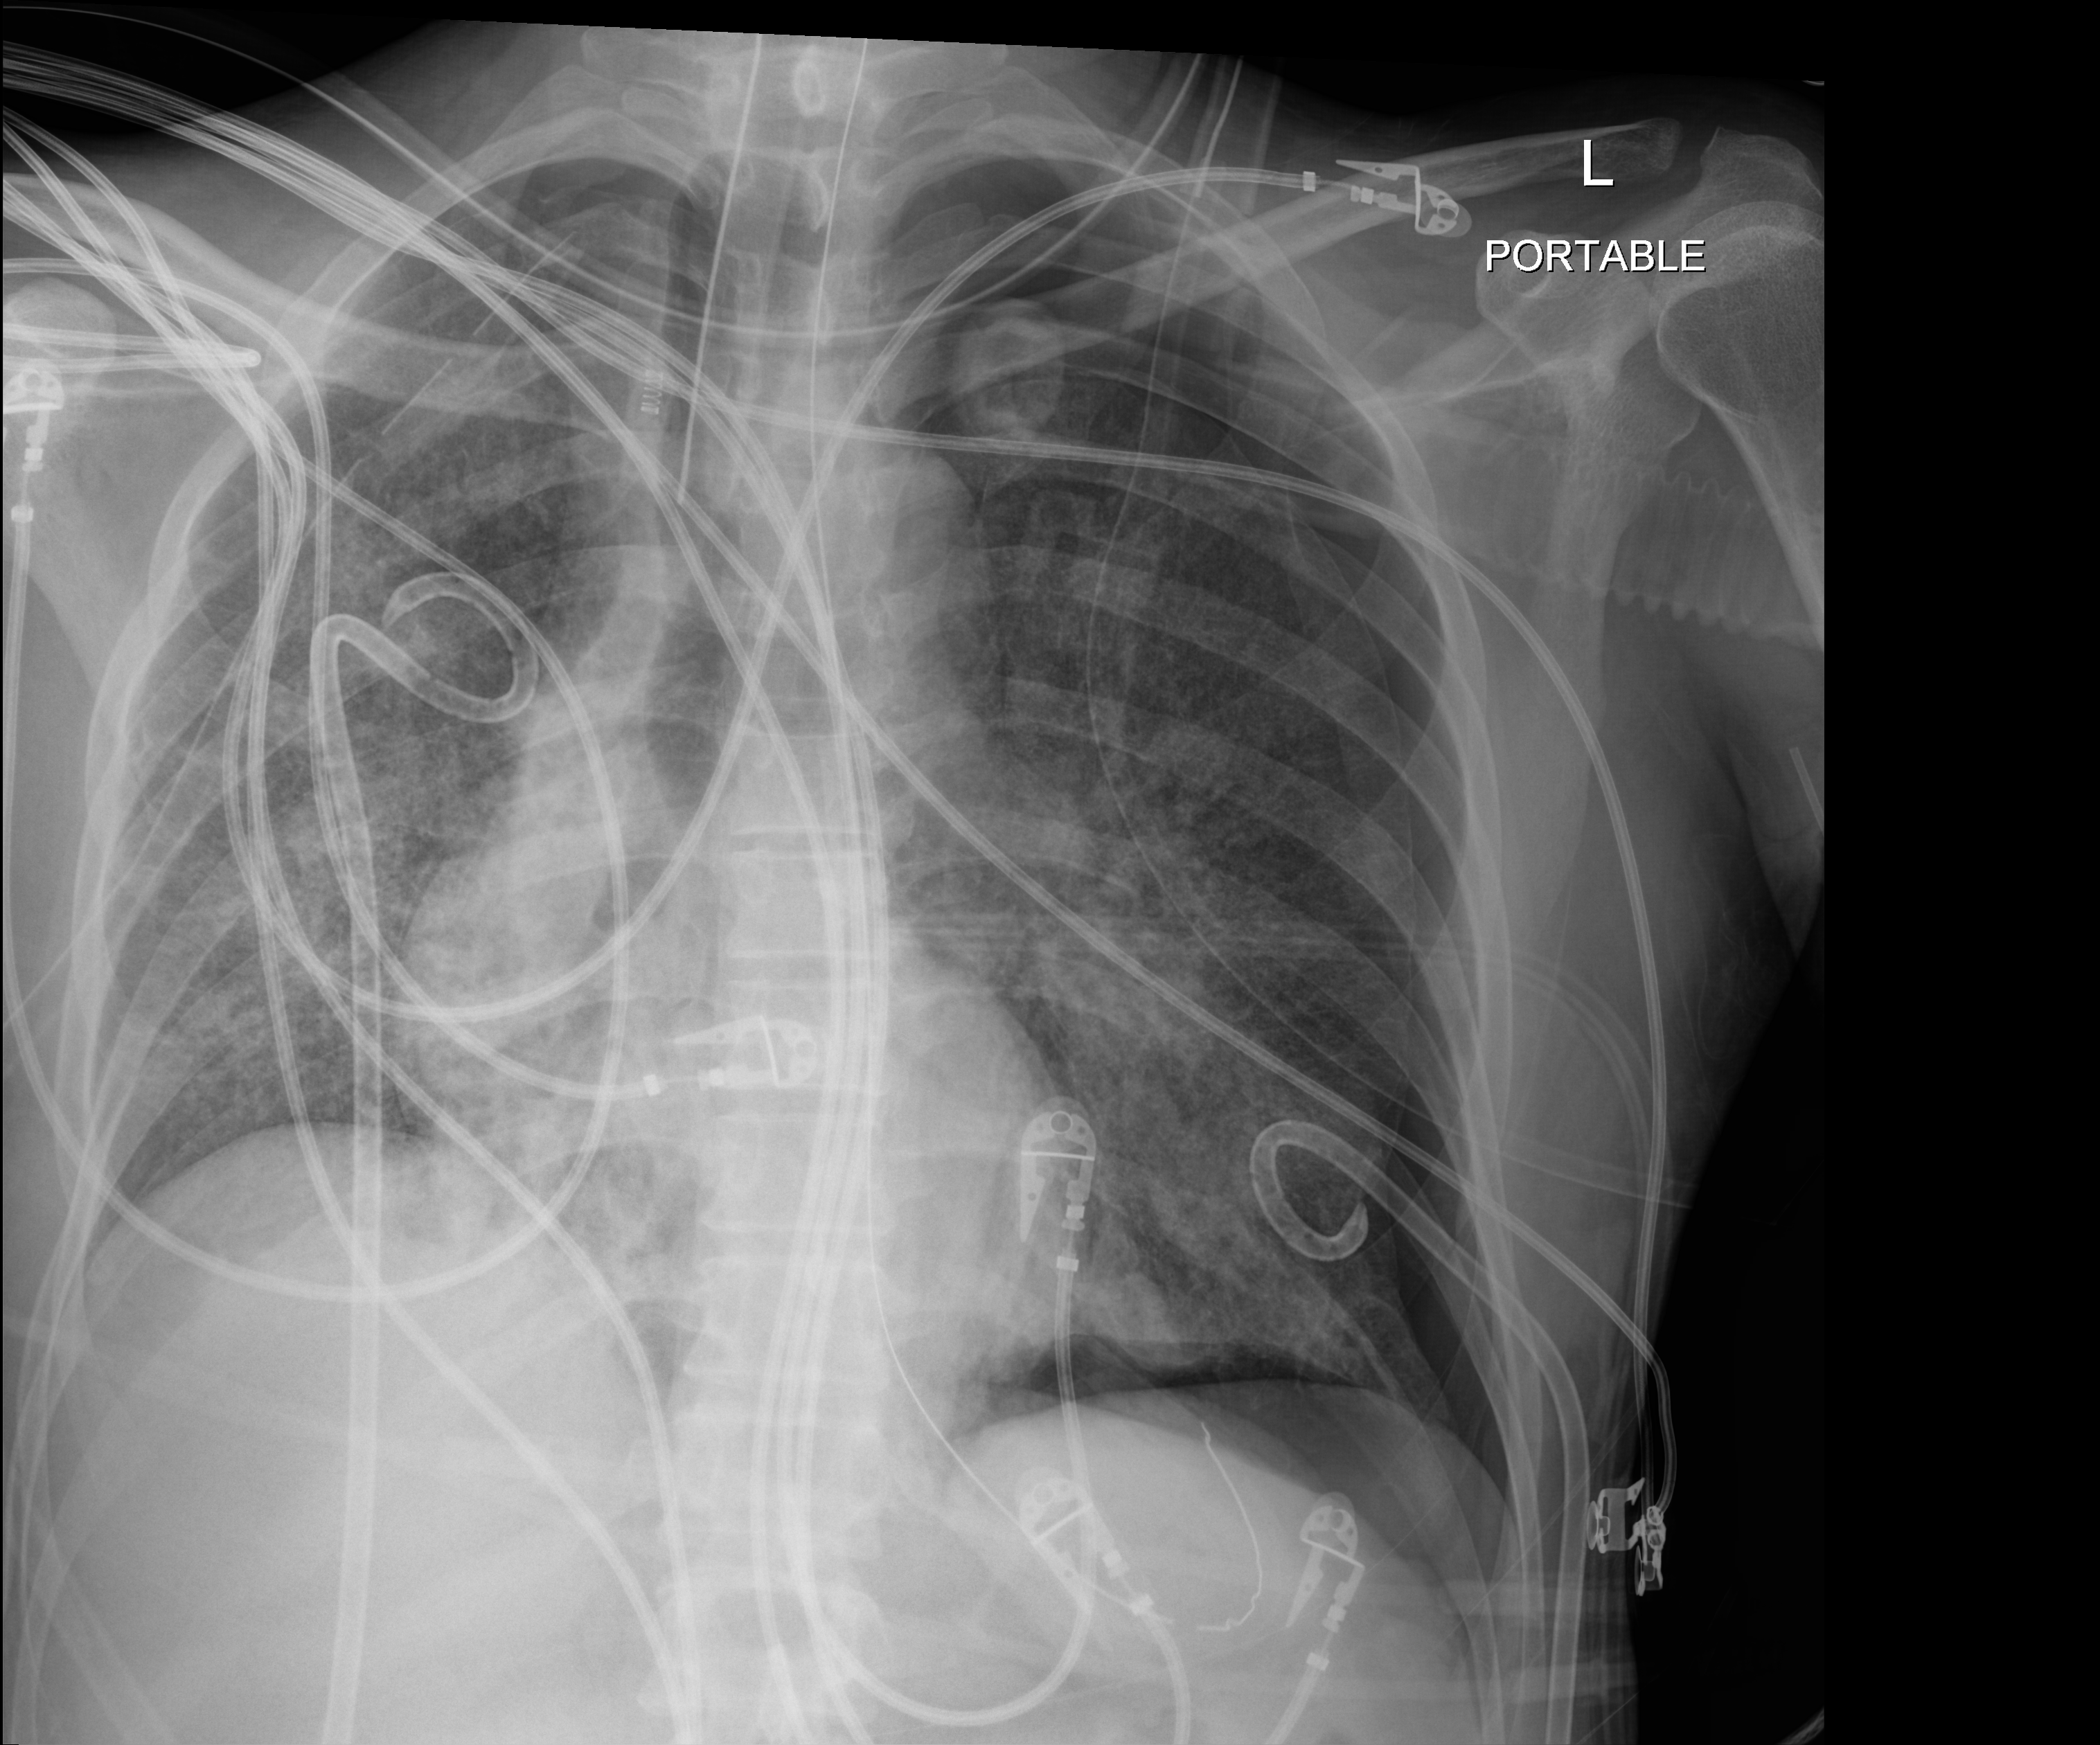
Chest X-ray, anteroposterior (AP) projection. Adult patient hospitalised with COVID-19, age 18–59 years.
Admission-level facts for this patient (not findings on this image; timing relative to this image not recorded):
- mechanically ventilated during this hospital stay: yes
- admitted to intensive care during this hospital stay: yes